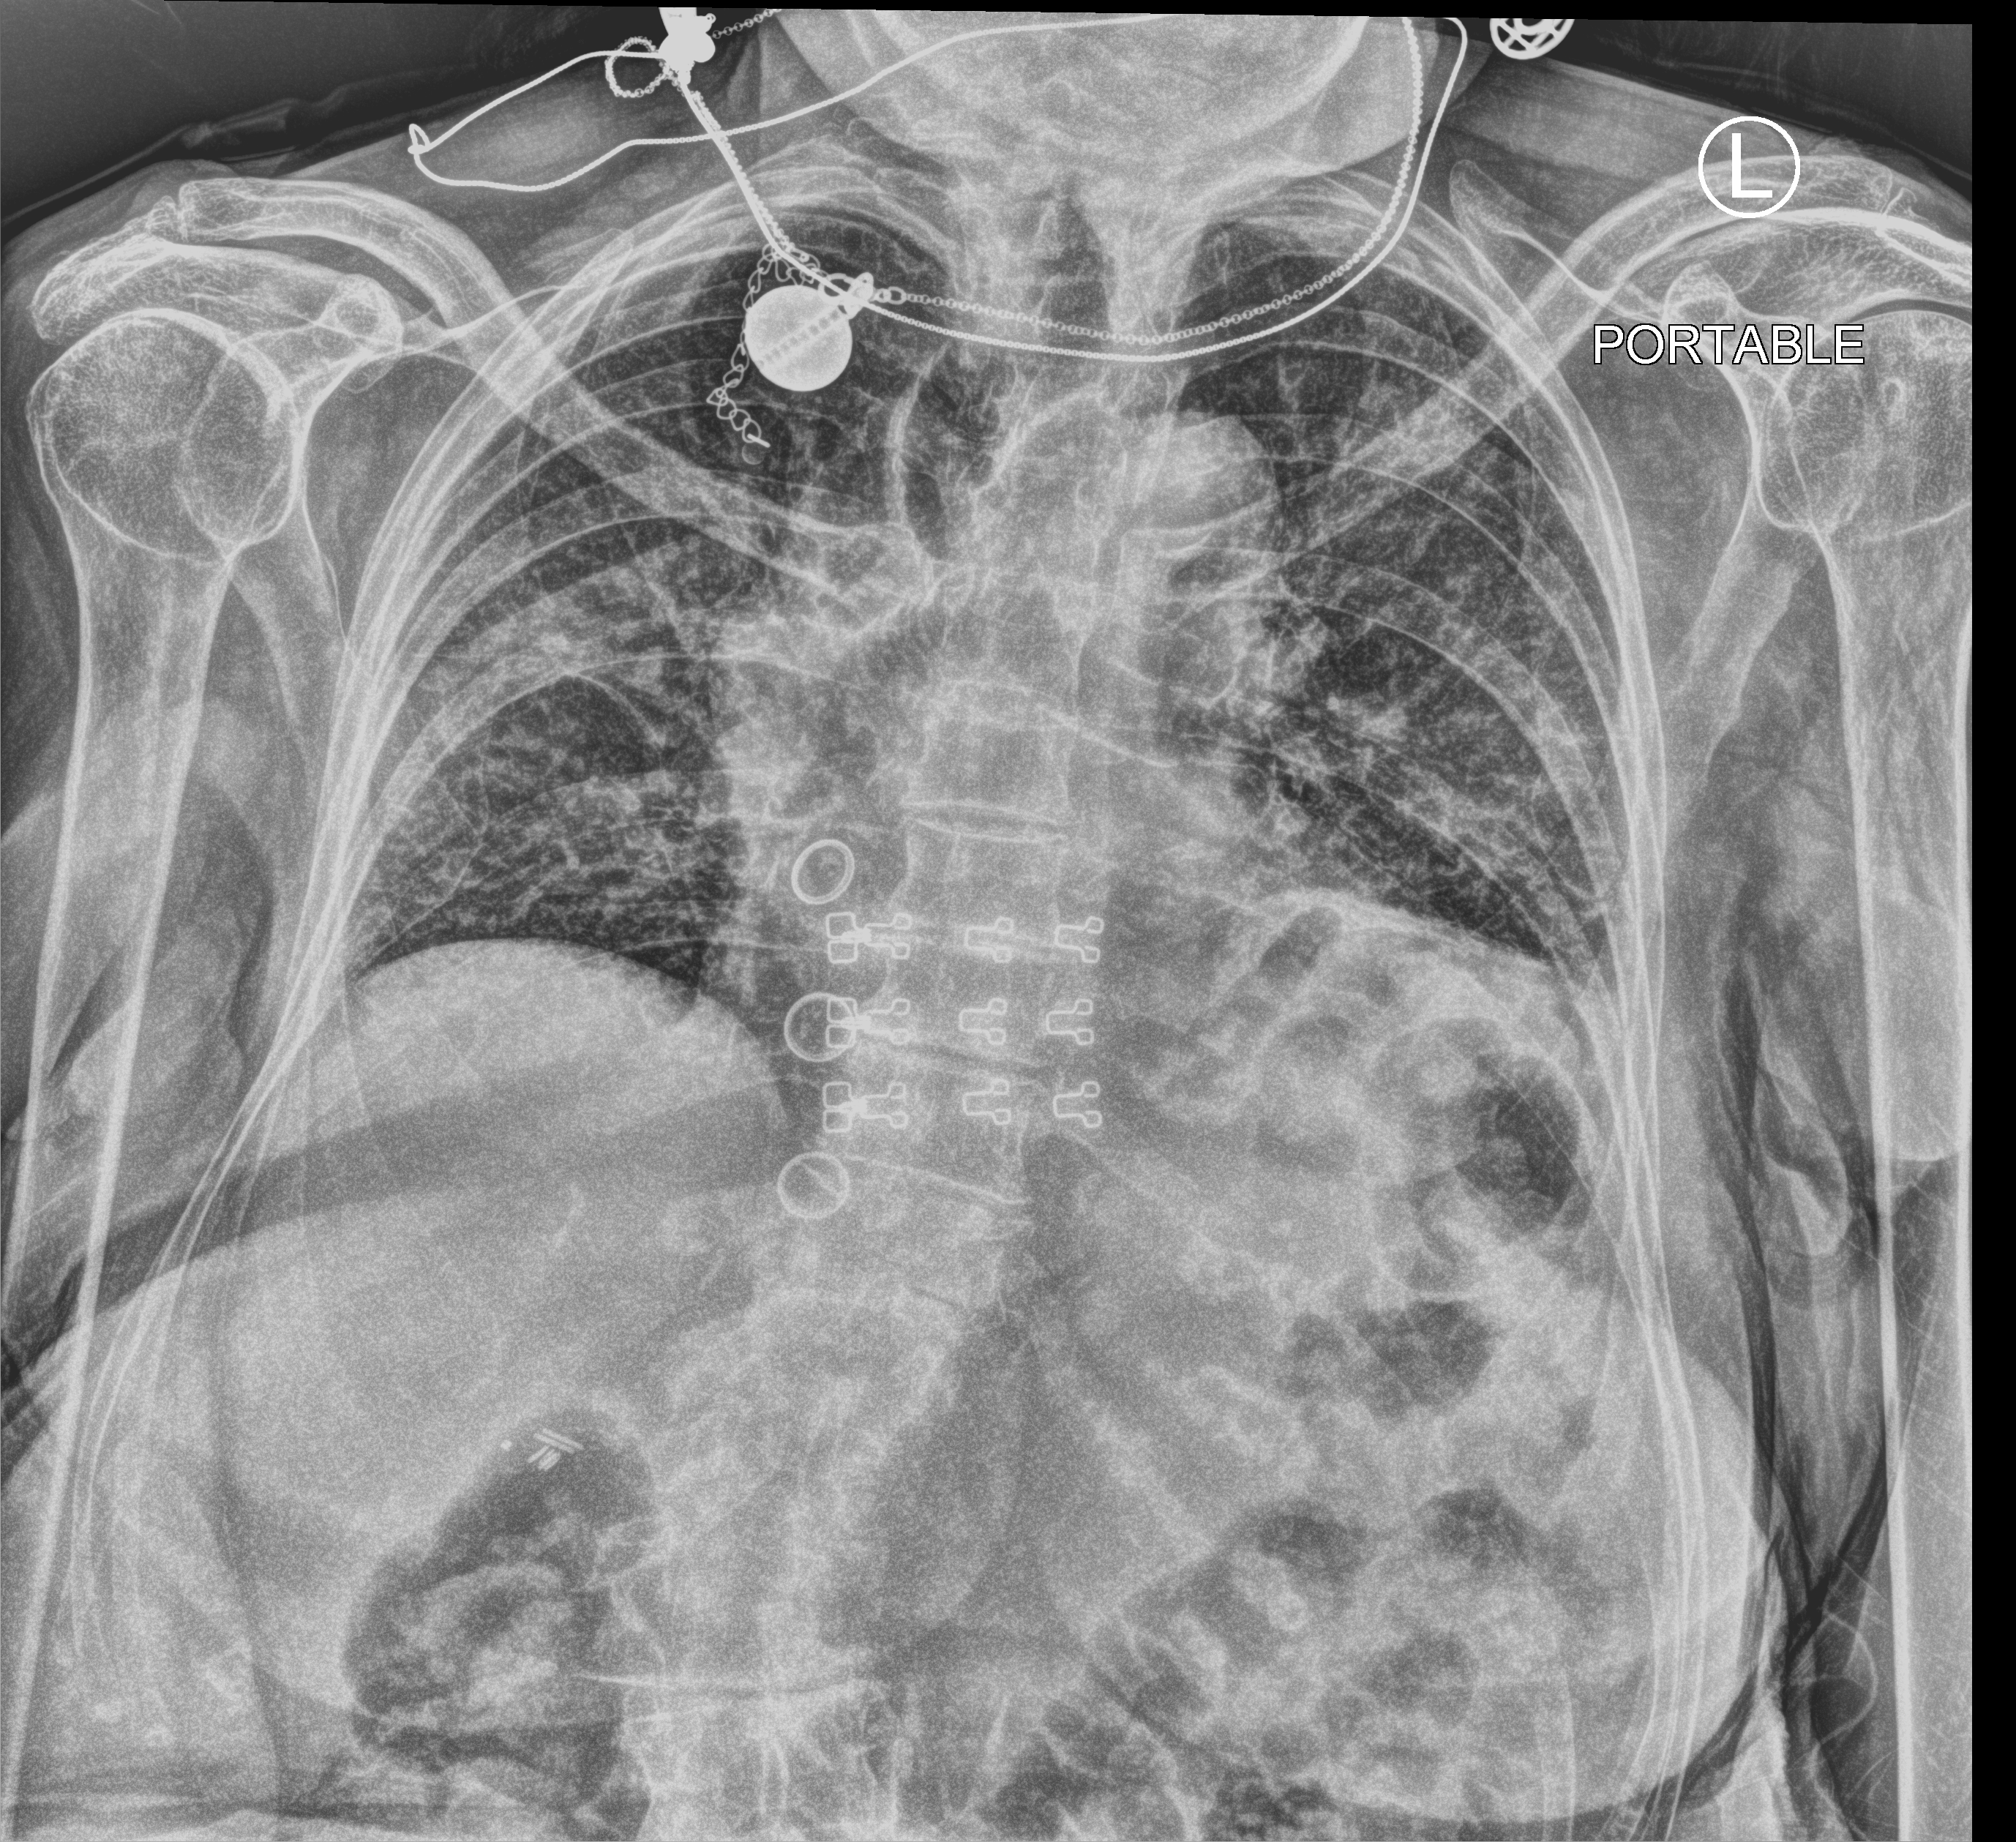
Portable chest radiograph; anteroposterior (AP) projection. Patient hospitalised with COVID-19; female, aged 75–90 years.
From the hospital-stay record, not from the radiograph (when in the stay this image was taken is not recorded):
- mechanically ventilated during this hospital stay: no
- length of hospital stay: 1 day
- admitted to intensive care during this hospital stay: no